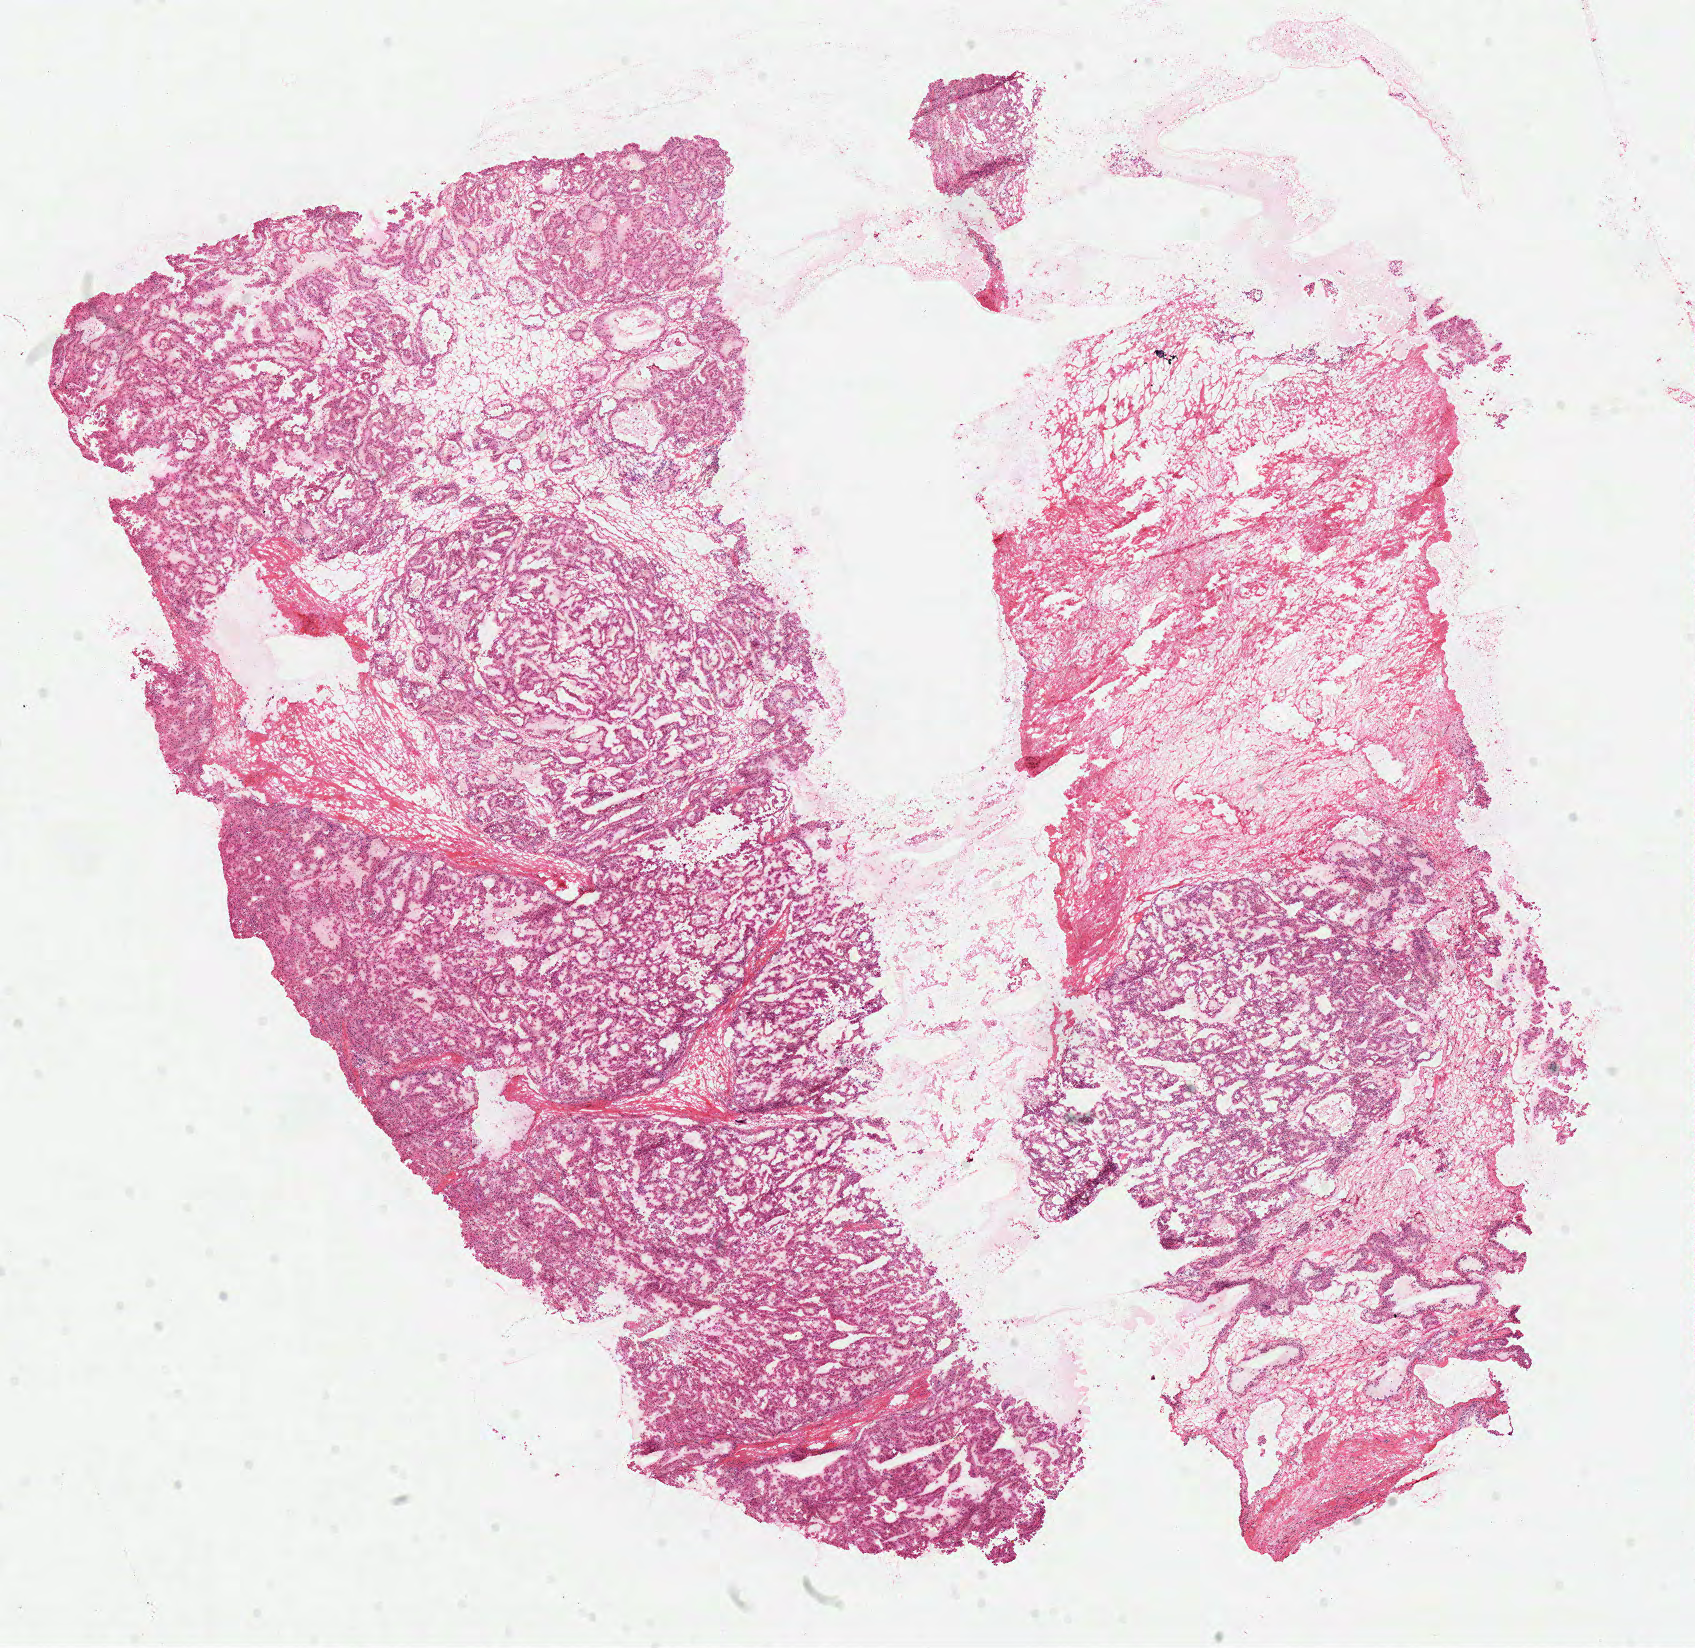
H&E-stained whole-slide image — a low-resolution overview of the entire scanned area, about 13.4 x 13.0 mm (slide scanned at 40x). Frozen section. Sample: primary tumour, kidney. Male, age 51 years at initial diagnosis. Slide review estimates, as recorded: tumour cells 60%, tumour nuclei 80%, normal cells 0%, stromal cells 40%, necrosis 0%.
TNM: T1b N0 M0. Laterality: left. Histologic diagnosis: Papillary adenocarcinoma, NOS. AJCC pathologic stage: I.